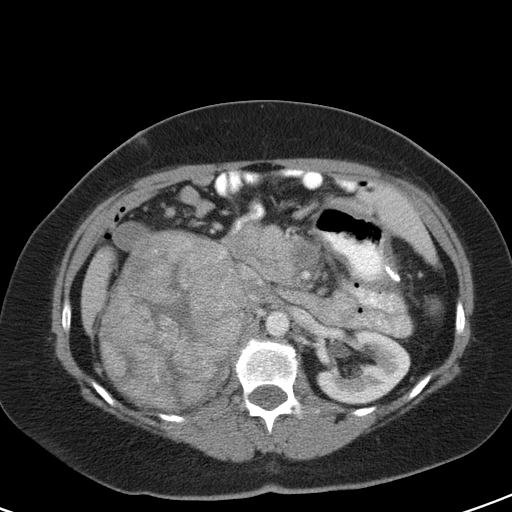
Contrast-enhanced abdominal CT, one axial slice; slice 65 of 126 in the series (ordered by position); 120 kVp; intravenous contrast given; soft-tissue window (W 400 / L 40 HU); 512 × 512 image matrix, field of view 356 × 356 mm. Female patient, age 51 years. From the clinical record (not read from this slice): diagnosis: adrenocortical carcinoma; tumour side: right adrenal; tumour size at pathology: 17 cm; Ki-67 index: 12 %; stage (as recorded): 2.
Annotated regions visible in this slice (semi-automatic segmentation, software-assisted and operator-edited):
- mass: bounding box [x1, y1, x2, y2] px = [100, 226, 243, 408]